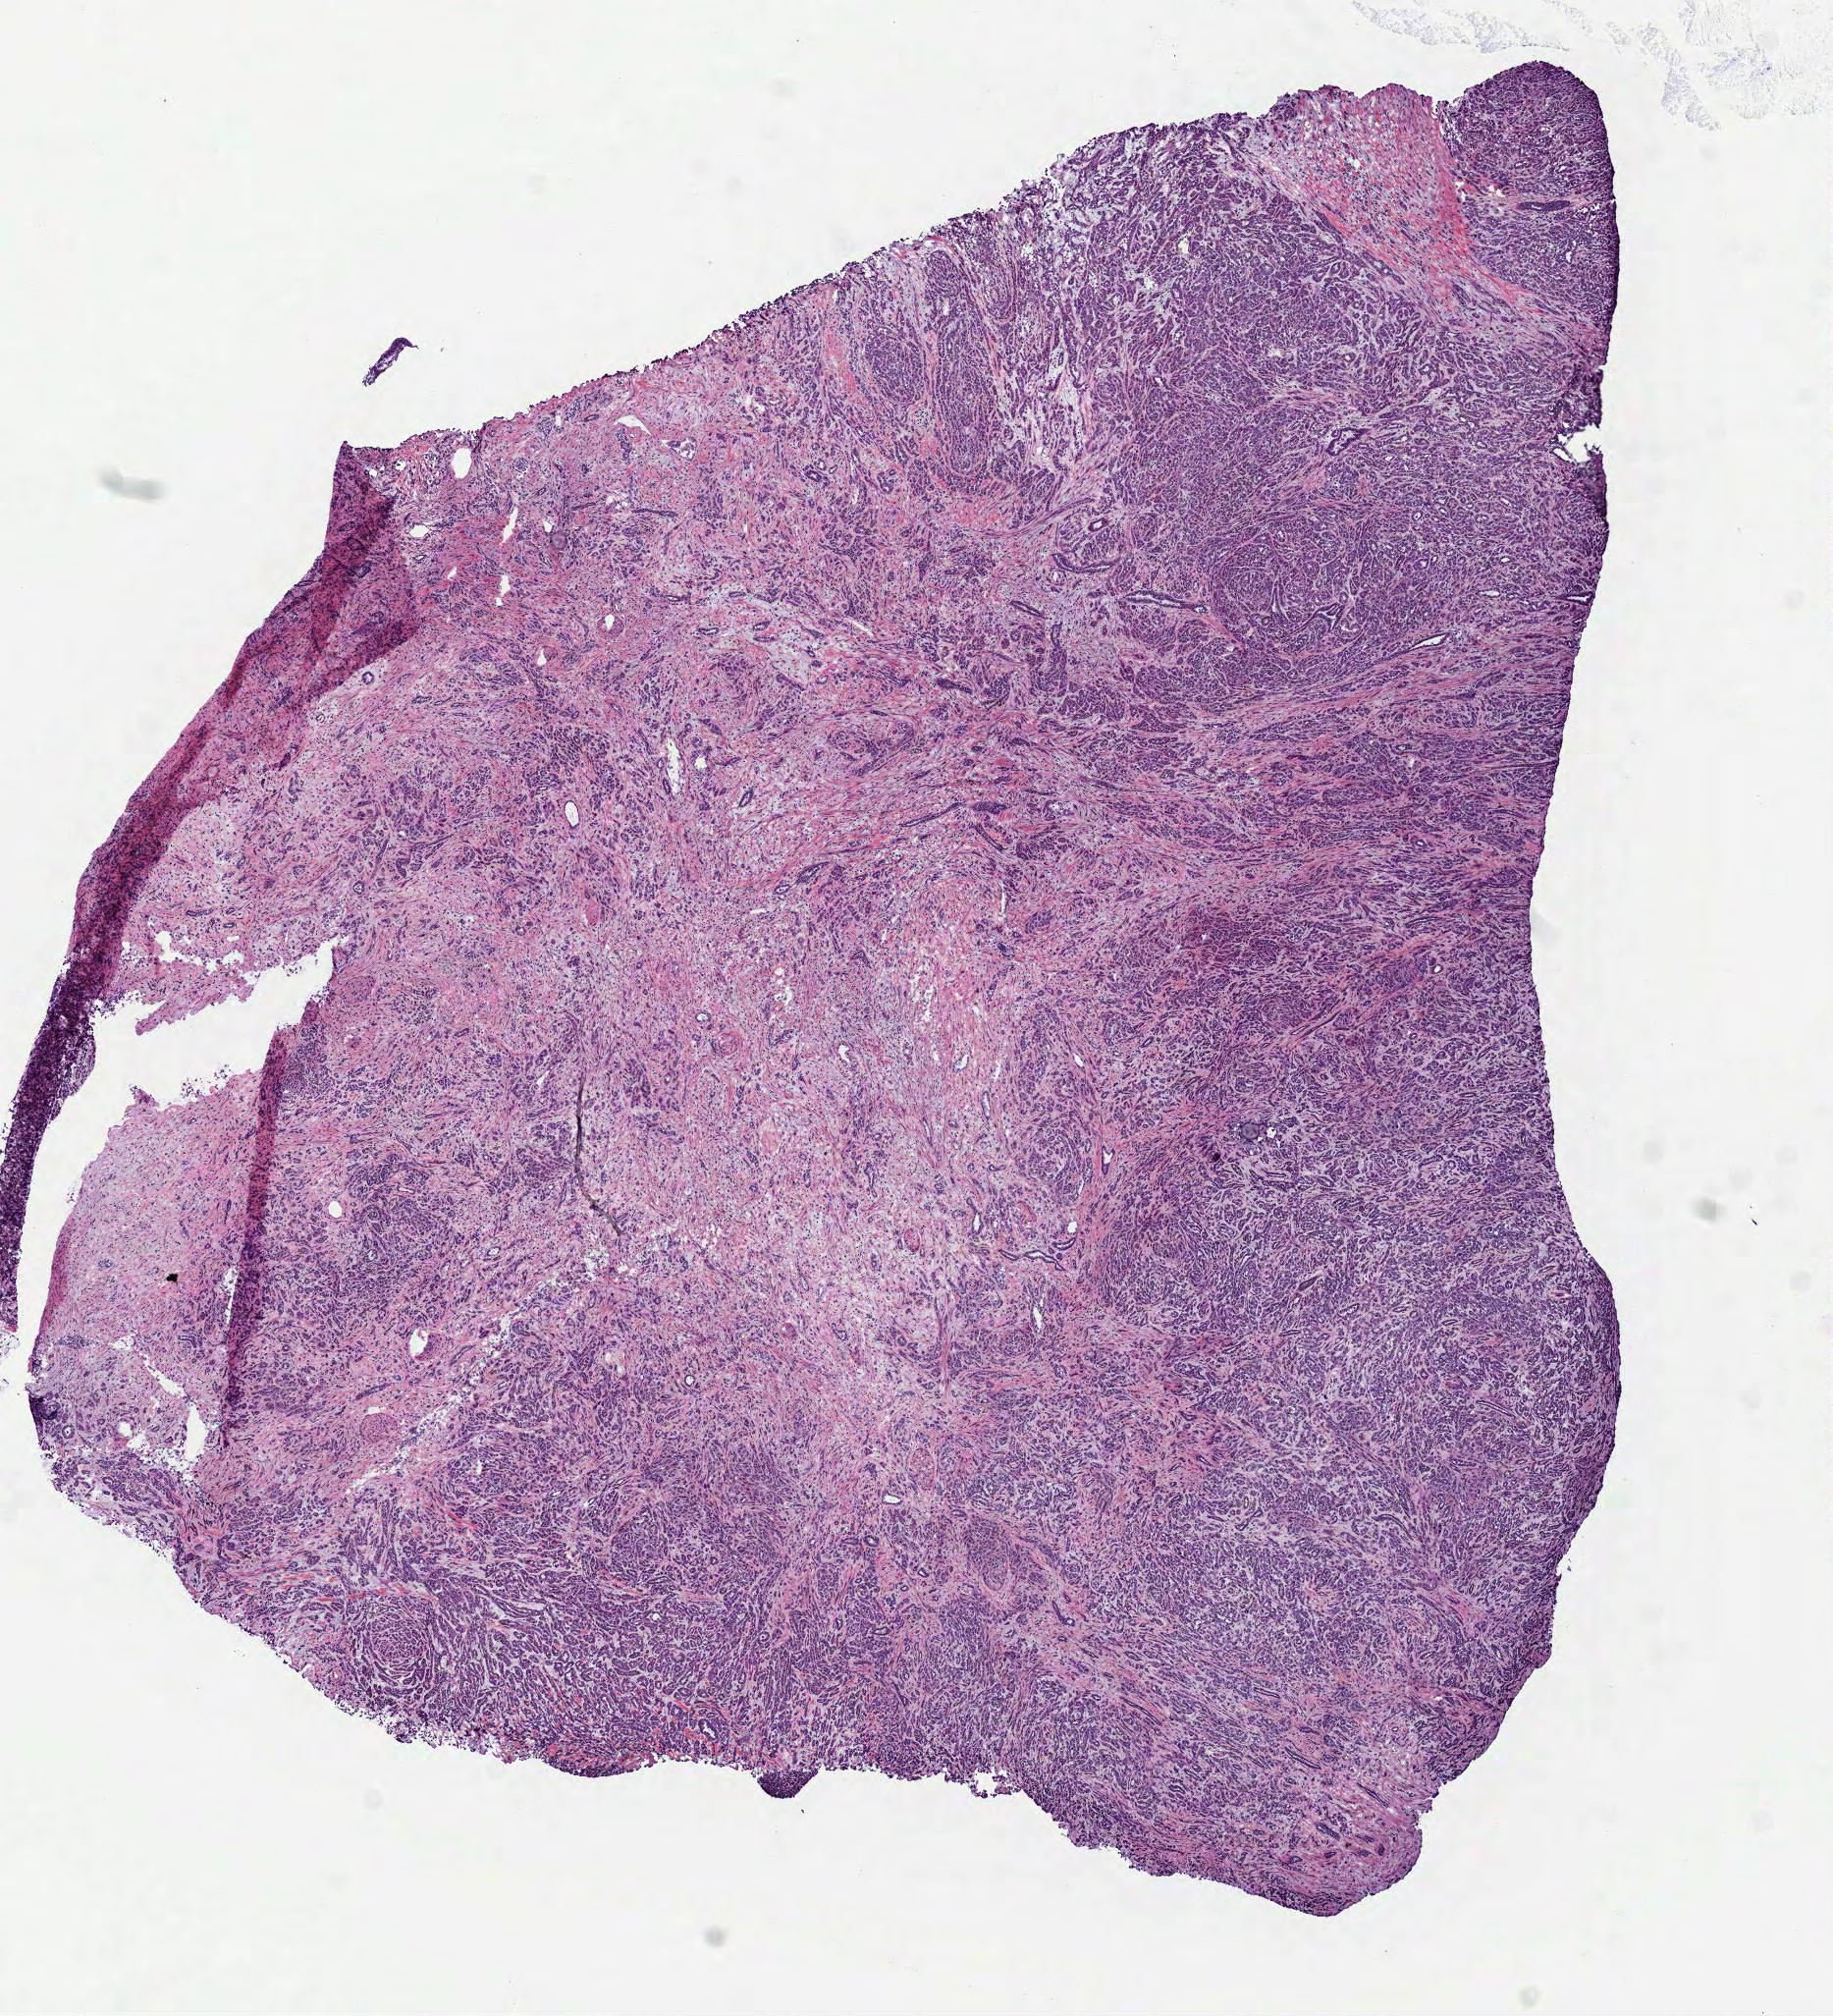
Whole-slide histology image, Hematoxylin and eosin (H&E) stained — whole scanned area (about 7.5 x 8.3 mm, acquisition: 40x scan) shown as a low-resolution overview, frozen section, primary tumour sample from the kidney. Patient: female, age at initial diagnosis 28 years. Pathologist review of this section (percent, as recorded): tumour cells 100%, tumour nuclei 85%, normal cells 0%, stromal cells 0%, necrosis 0%. Infiltration values recorded for this section: lymphocyte infiltration 2%, monocyte infiltration 0%, neutrophil infiltration 0%.
TNM: T3 N1 MX. AJCC pathologic stage: III. Histologic diagnosis: Papillary adenocarcinoma, NOS.